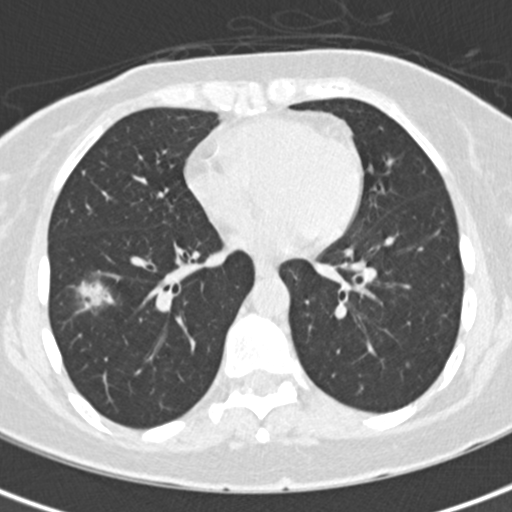
Axial slice from a low-dose chest CT screening exam; baseline screening round; lung window (W 1500 / L -600 HU); 2 mm slice thickness; 120 kVp; slice 99 of 171 in the series. Female participant, aged 56 years at enrolment. Former smoker at enrolment.
Expert reader's lesion annotation, bounding box <65,271,128,327> (left, top, right, bottom; pixels). The screening reader recorded 5 non-calcified nodules or masses ≥4 mm on this exam (right lower lobe, right upper lobe, left upper lobe, left lower lobe, left lower lobe); which of them this box marks is not recorded. Participant outcome: lung cancer diagnosed 26 days after this screen — bronchiolo-alveolar carcinoma, mucinous, right lower lobe, well differentiated (G1), stage IA (AJCC 6th edition), 19 mm at pathology.